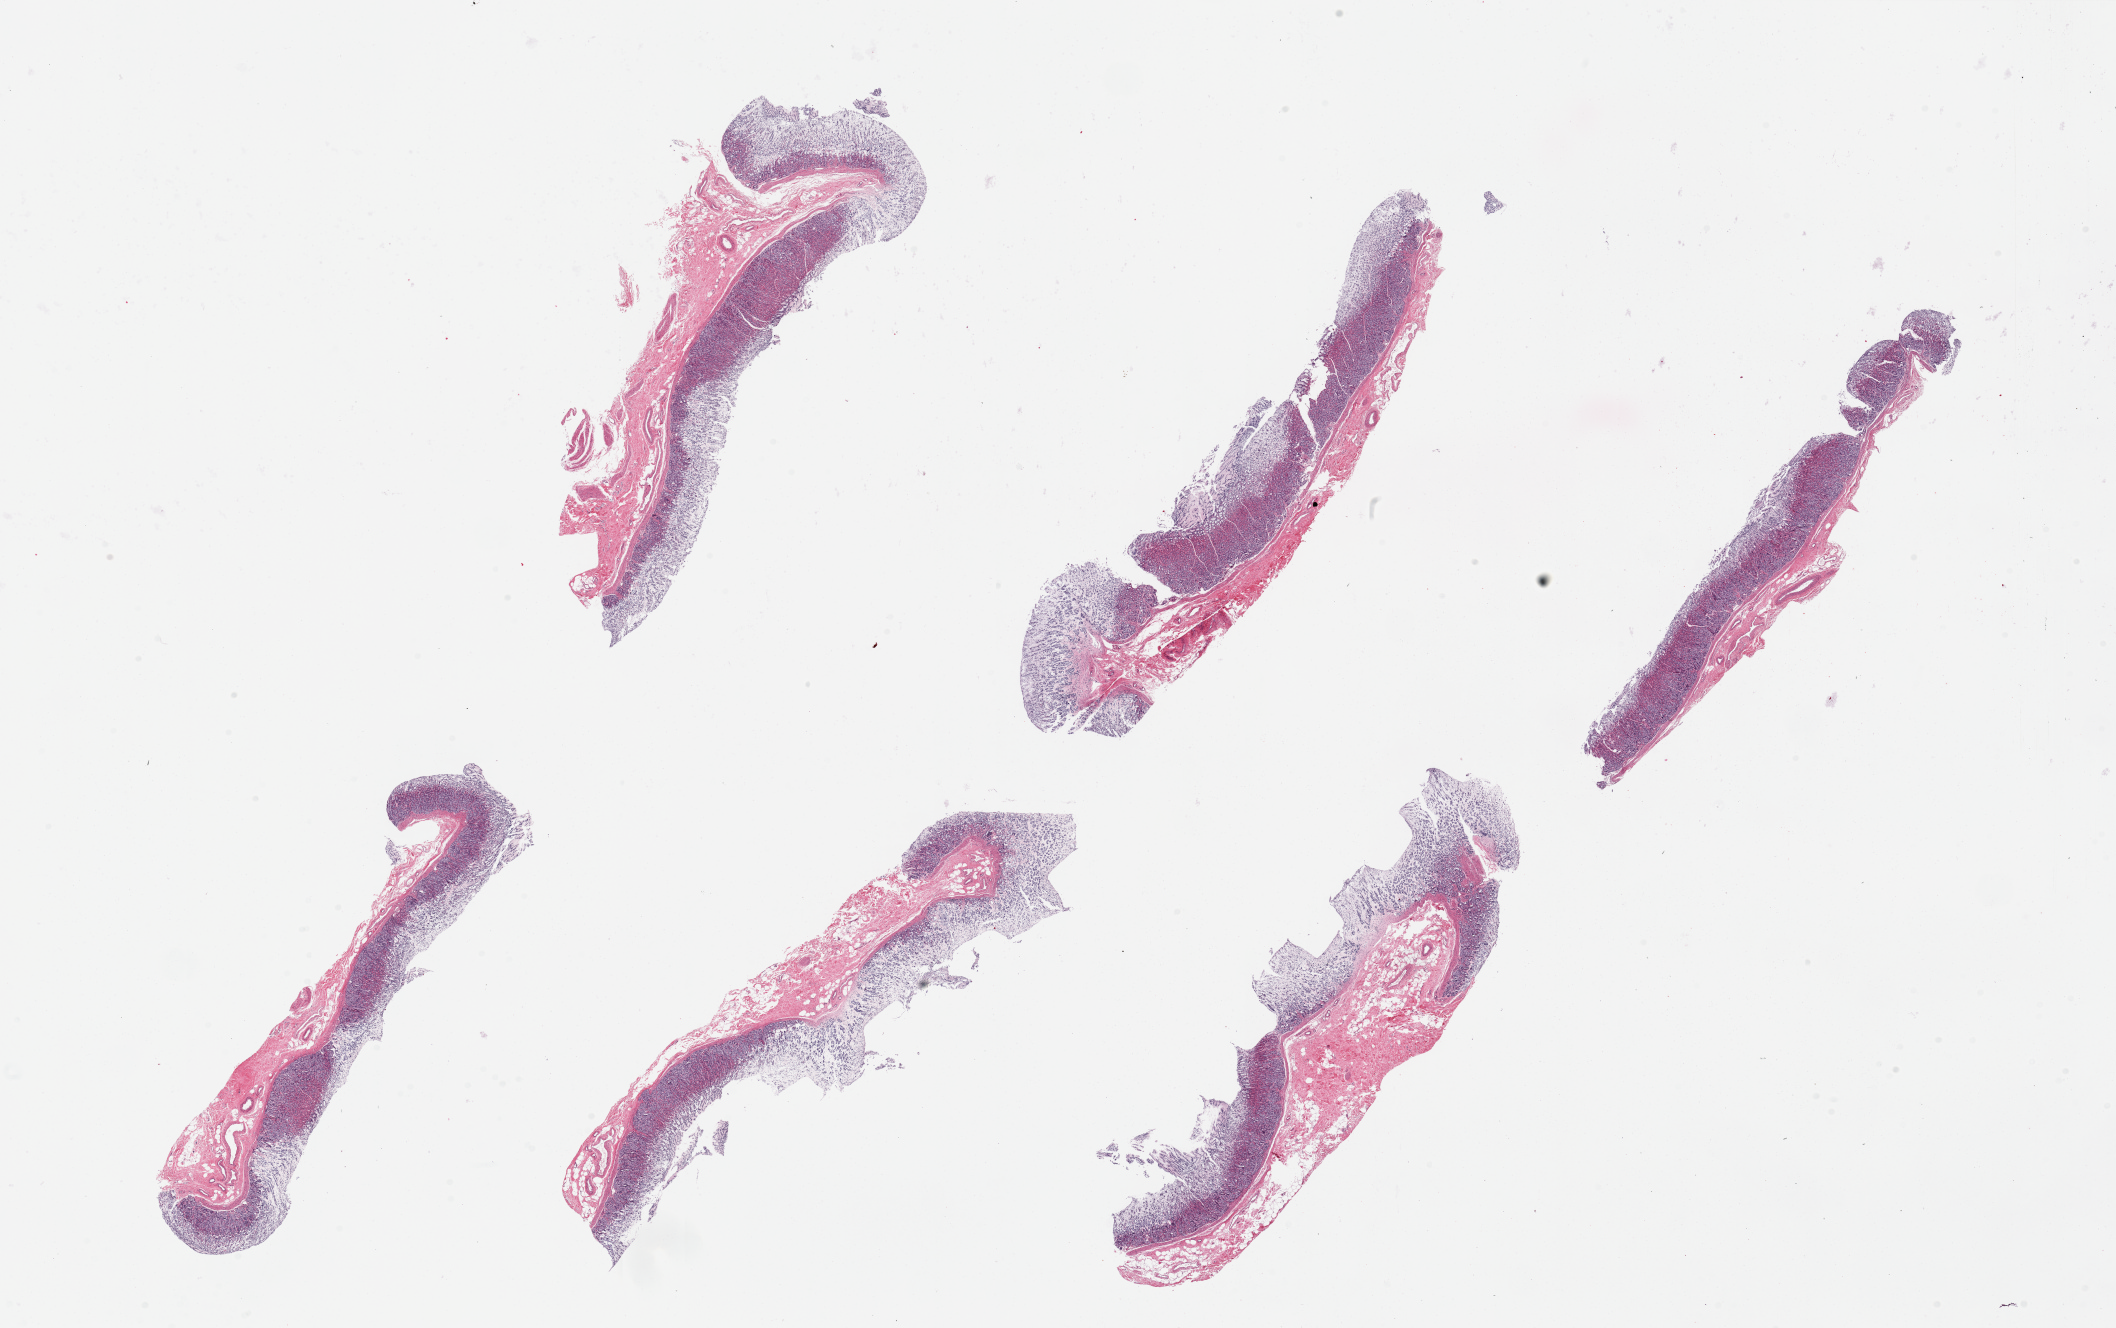
H&E whole-slide image, brightfield — shown as a low-resolution overview of the whole scanned area (about 33.5 x 21.0 mm), PAXgene-fixed, paraffin-embedded tissue, target tissue: stomach, tissue donor sample. Donor sex: male.
Review note (as recorded): 1 piece; comparable to 25 block.